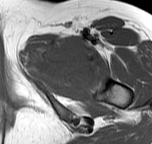
MRI of an extremity soft-tissue mass, one axial slice. Position 45 of 57 along the scan axis. MR volume resampled by the dataset authors to the PET/CT grid (not the native acquisition matrix). 152 × 144 image matrix. Female patient. Case-level facts recorded for this patient, not image findings: histological type: pleiomorphic leiomyosarcoma; grade: intermediate; site of the primary tumour: left thigh.
Annotated regions visible in this slice (expert contour drawn on MRI and transferred to this co-registered scan by the dataset authors):
- gross tumour volume including surrounding oedema: box from (x=25, y=35) to (x=92, y=86) px
- gross tumour volume (mass): (x=43, y=39)–(x=92, y=84)